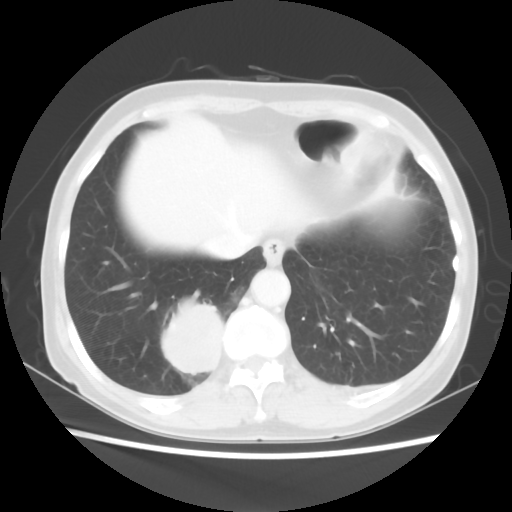
Chest CT, one axial slice. Position 13 of 56 along the scan axis. Reconstruction kernel STANDARD. Lung window (W 1500 / L -600 HU). 5 mm slice thickness. 512 × 512 image matrix, field of view 332 × 332 mm. Patient: female, 66 years. Case-level facts recorded for this patient, not image findings: clinical TNM (as recorded): T2 N3 M0; histopathological grade: G3.
Structures marked on this image (rectangle marked by the reading radiologist):
- lung tumour (recorded histology: small cell carcinoma): box from (x=157, y=294) to (x=231, y=392) px